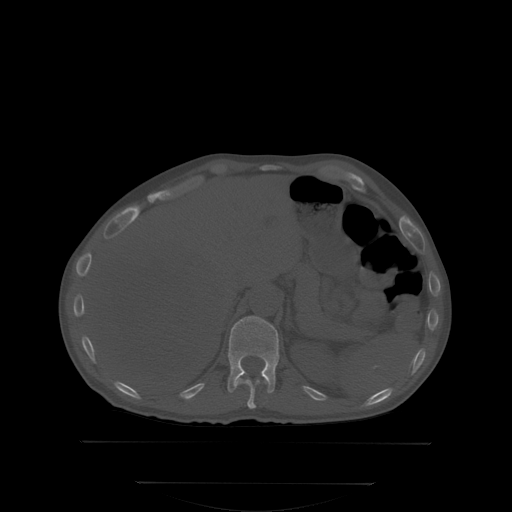
CT including the spine, one axial slice. Position 172 of 350 along the scan axis. Bone window (W 1800 / L 400 HU). 2.5 mm slice thickness. 512 × 512 image matrix, field of view 500 × 500 mm. Male patient, age 58 years. Case-level facts recorded for this patient, not image findings: primary cancer: prostate.
Annotated regions visible in this slice (semi-automatically segmented with operator editing):
- T11 vertebra: bounding box [x1, y1, x2, y2] px = [239, 378, 266, 408]
- T12 vertebra: [228, 316, 279, 393]